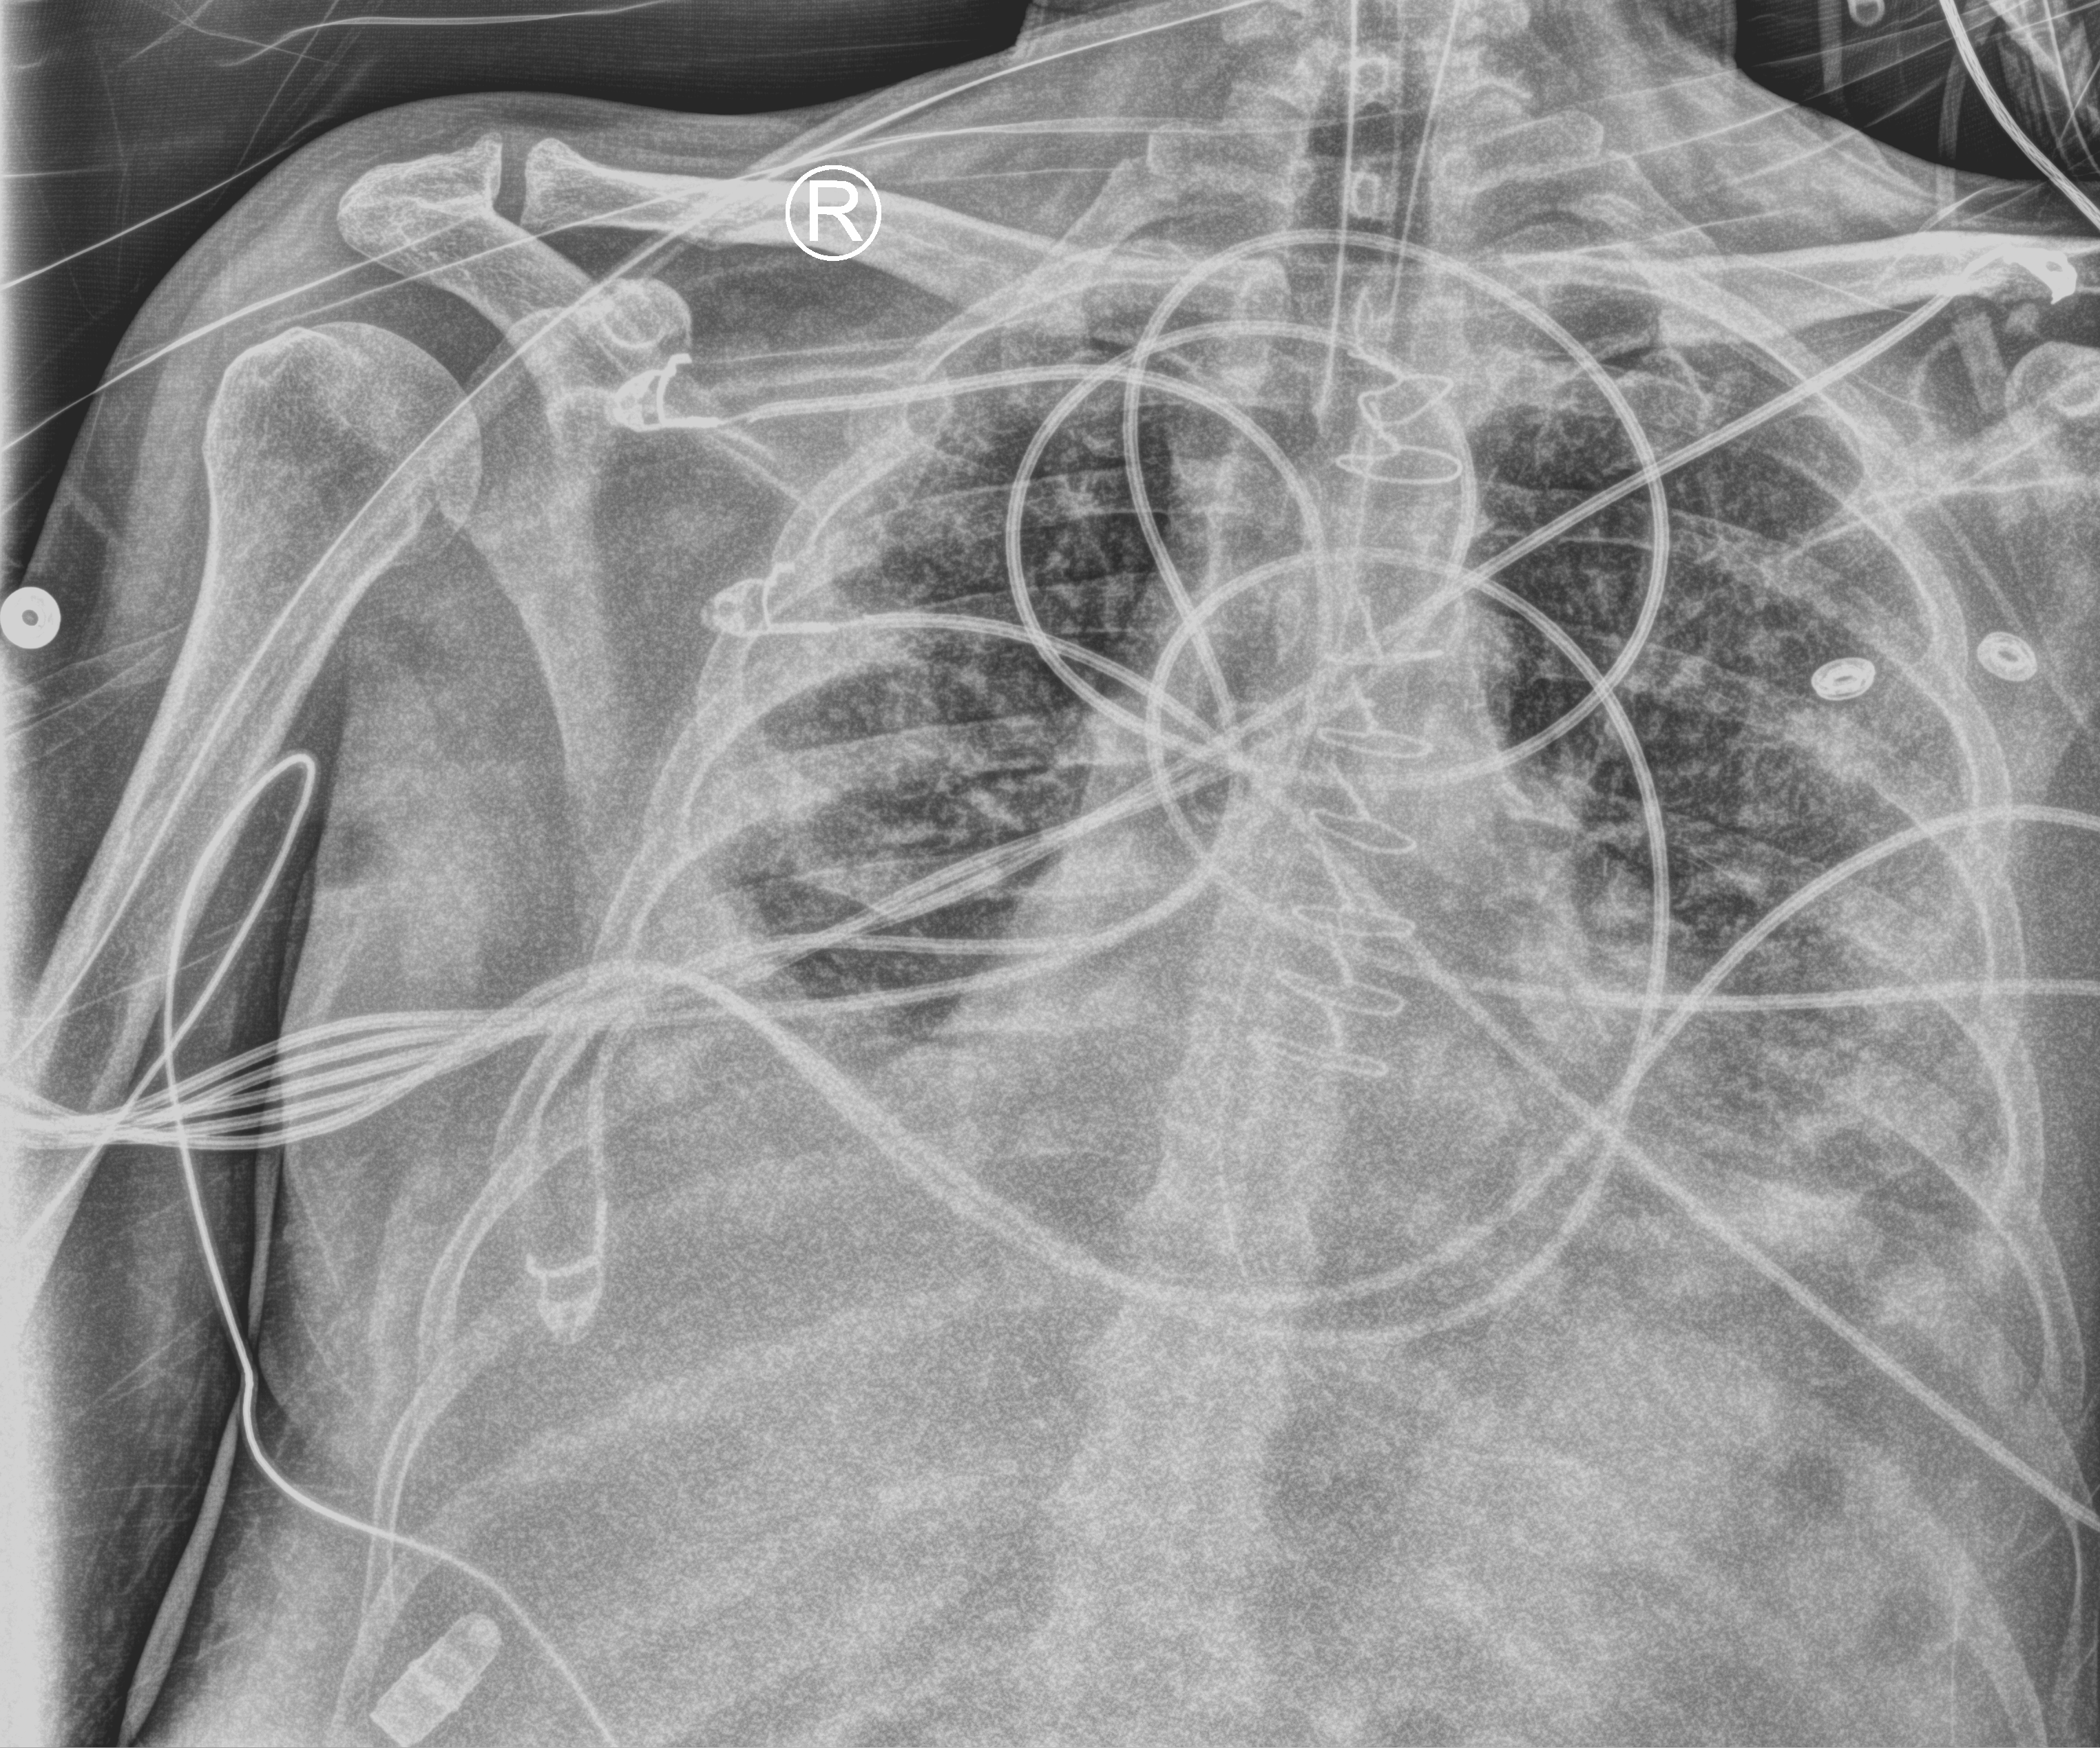
Chest X-ray (portable); anteroposterior (AP) projection. Male patient hospitalised with COVID-19, age 18–59 years.
Hospital-stay facts (about this admission, not read from this image; timing relative to this image not recorded): diabetes (admission record): yes; mechanically ventilated during this hospital stay: yes.